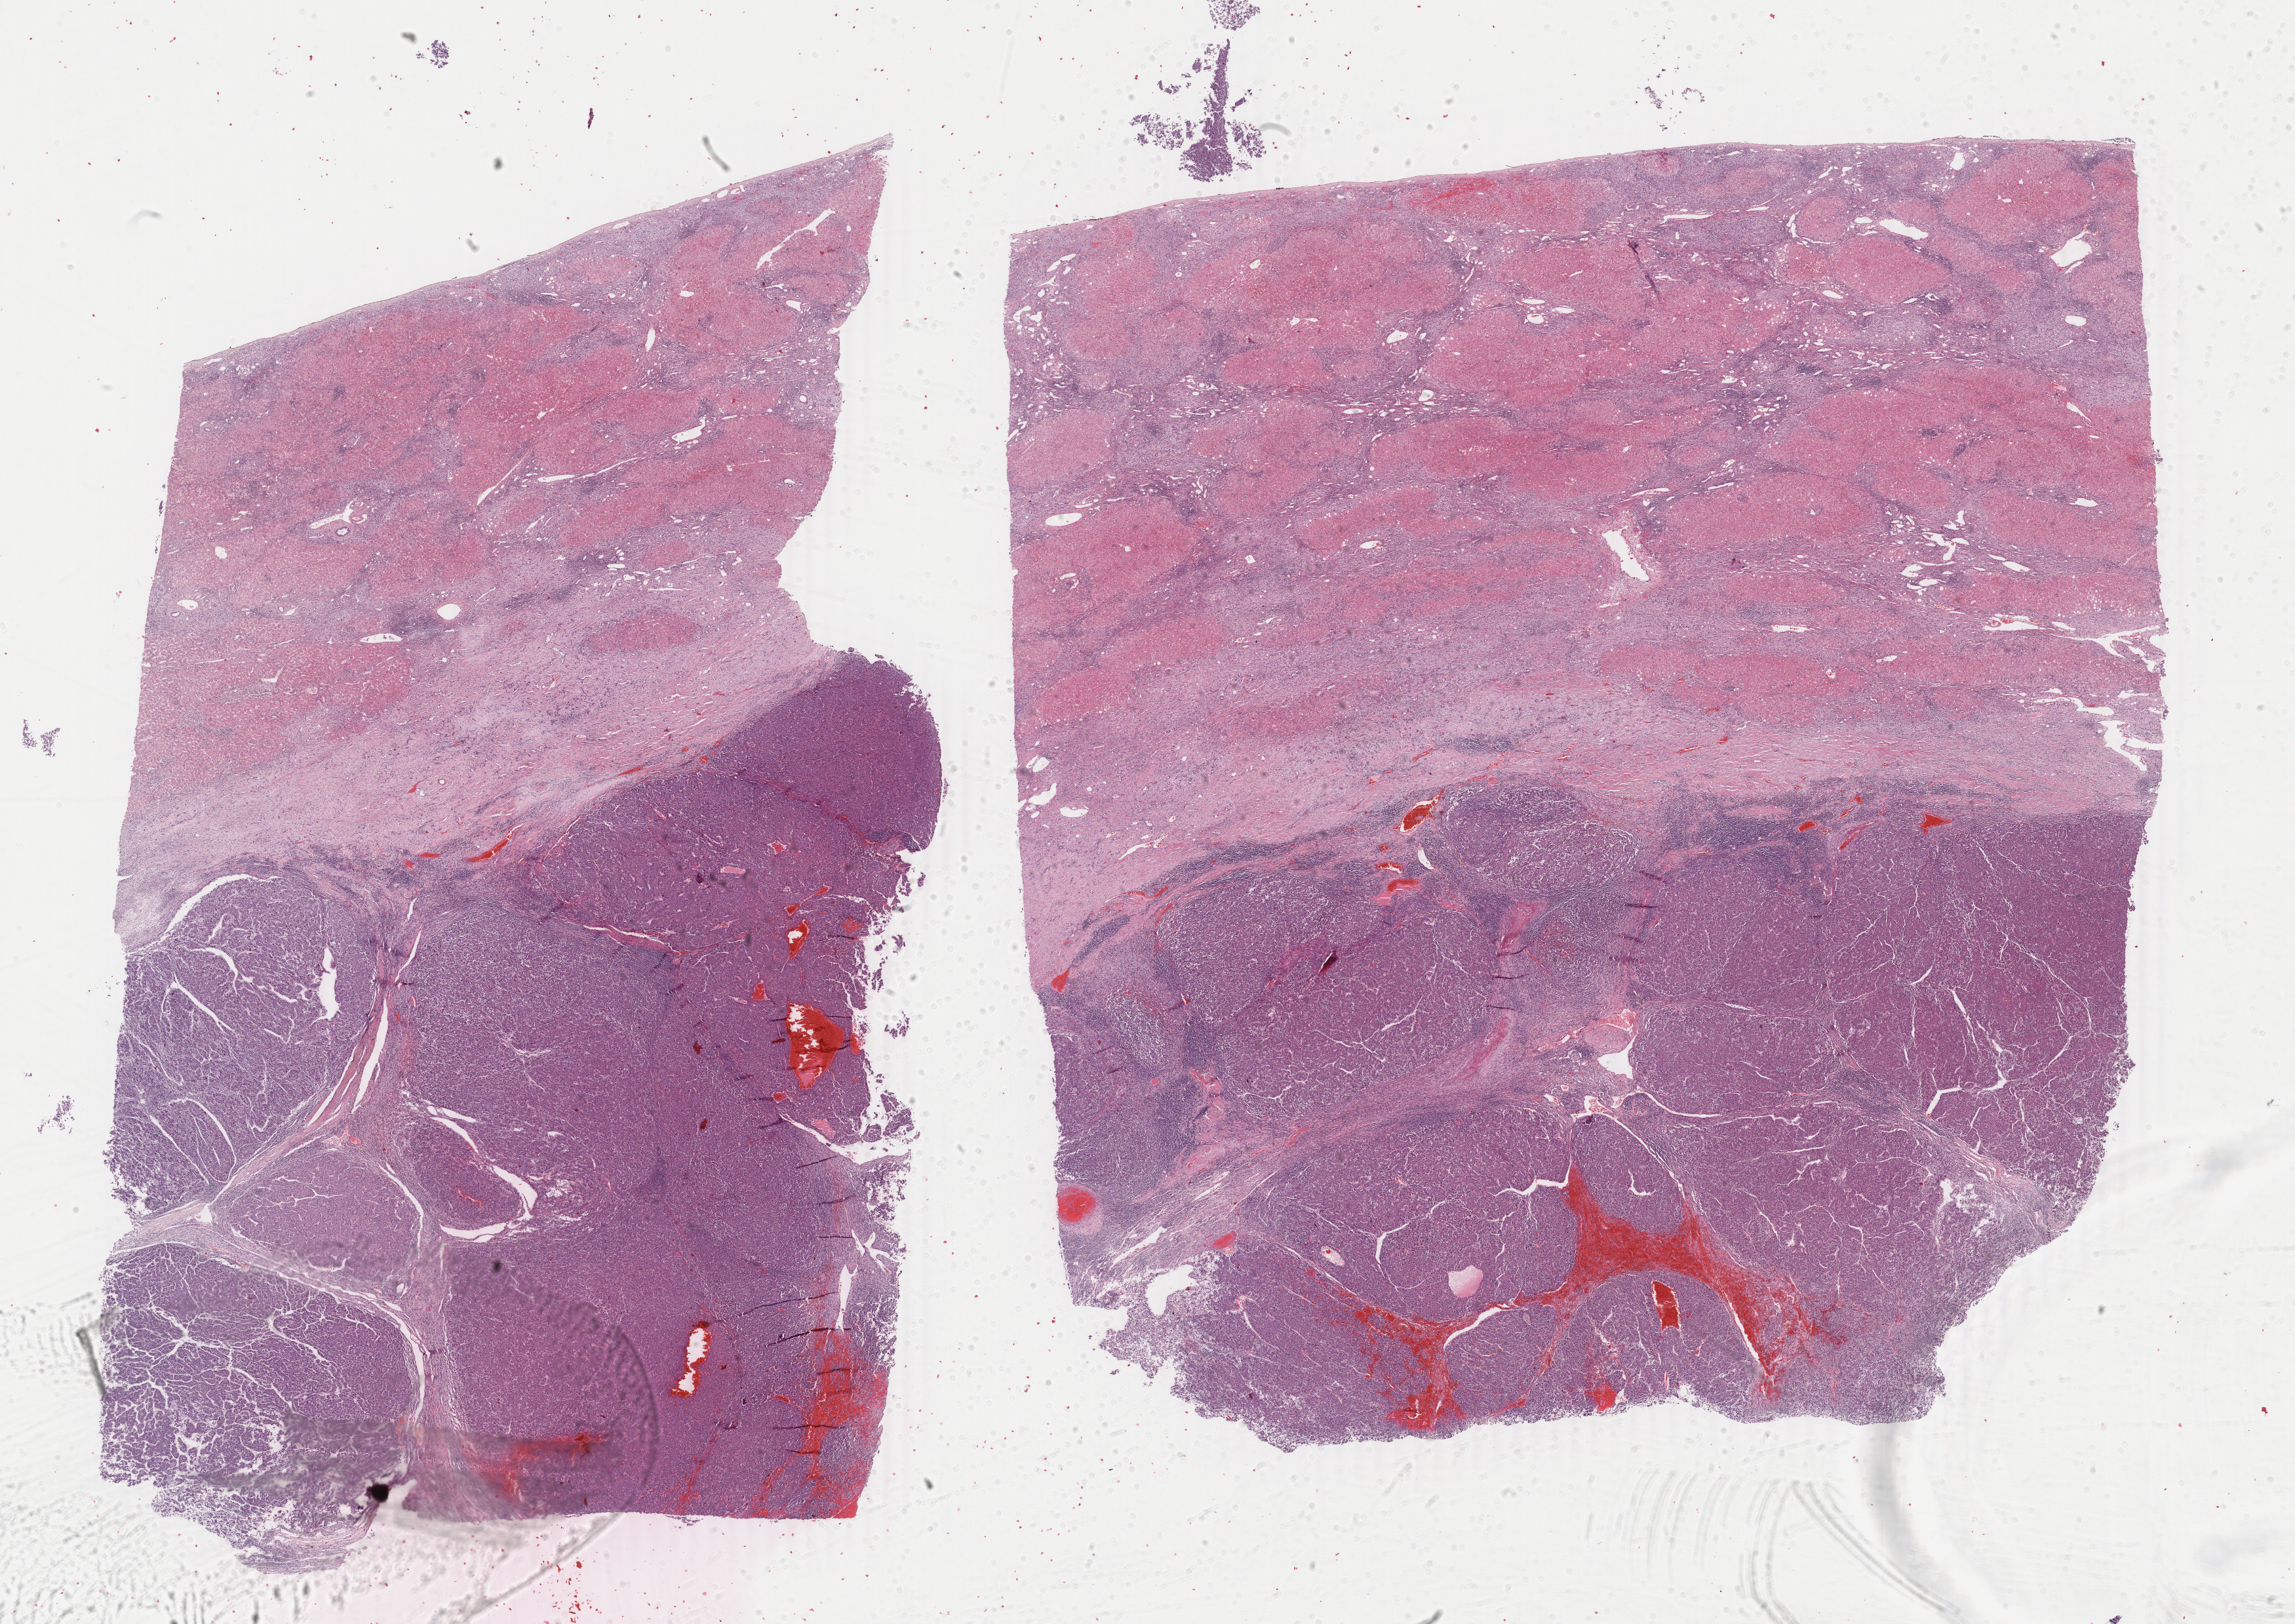
Digitized Hematoxylin and eosin (H&E) stained tissue section (whole slide), shown as a low-resolution overview of the whole scanned area (about 27.8 x 19.7 mm); FFPE section; sample: primary tumour, liver. Male, age 63 years at initial diagnosis. Histologic grade: G3 (poorly differentiated).
* diagnosis: Hepatocellular carcinoma, NOS
* AJCC pathologic stage: I